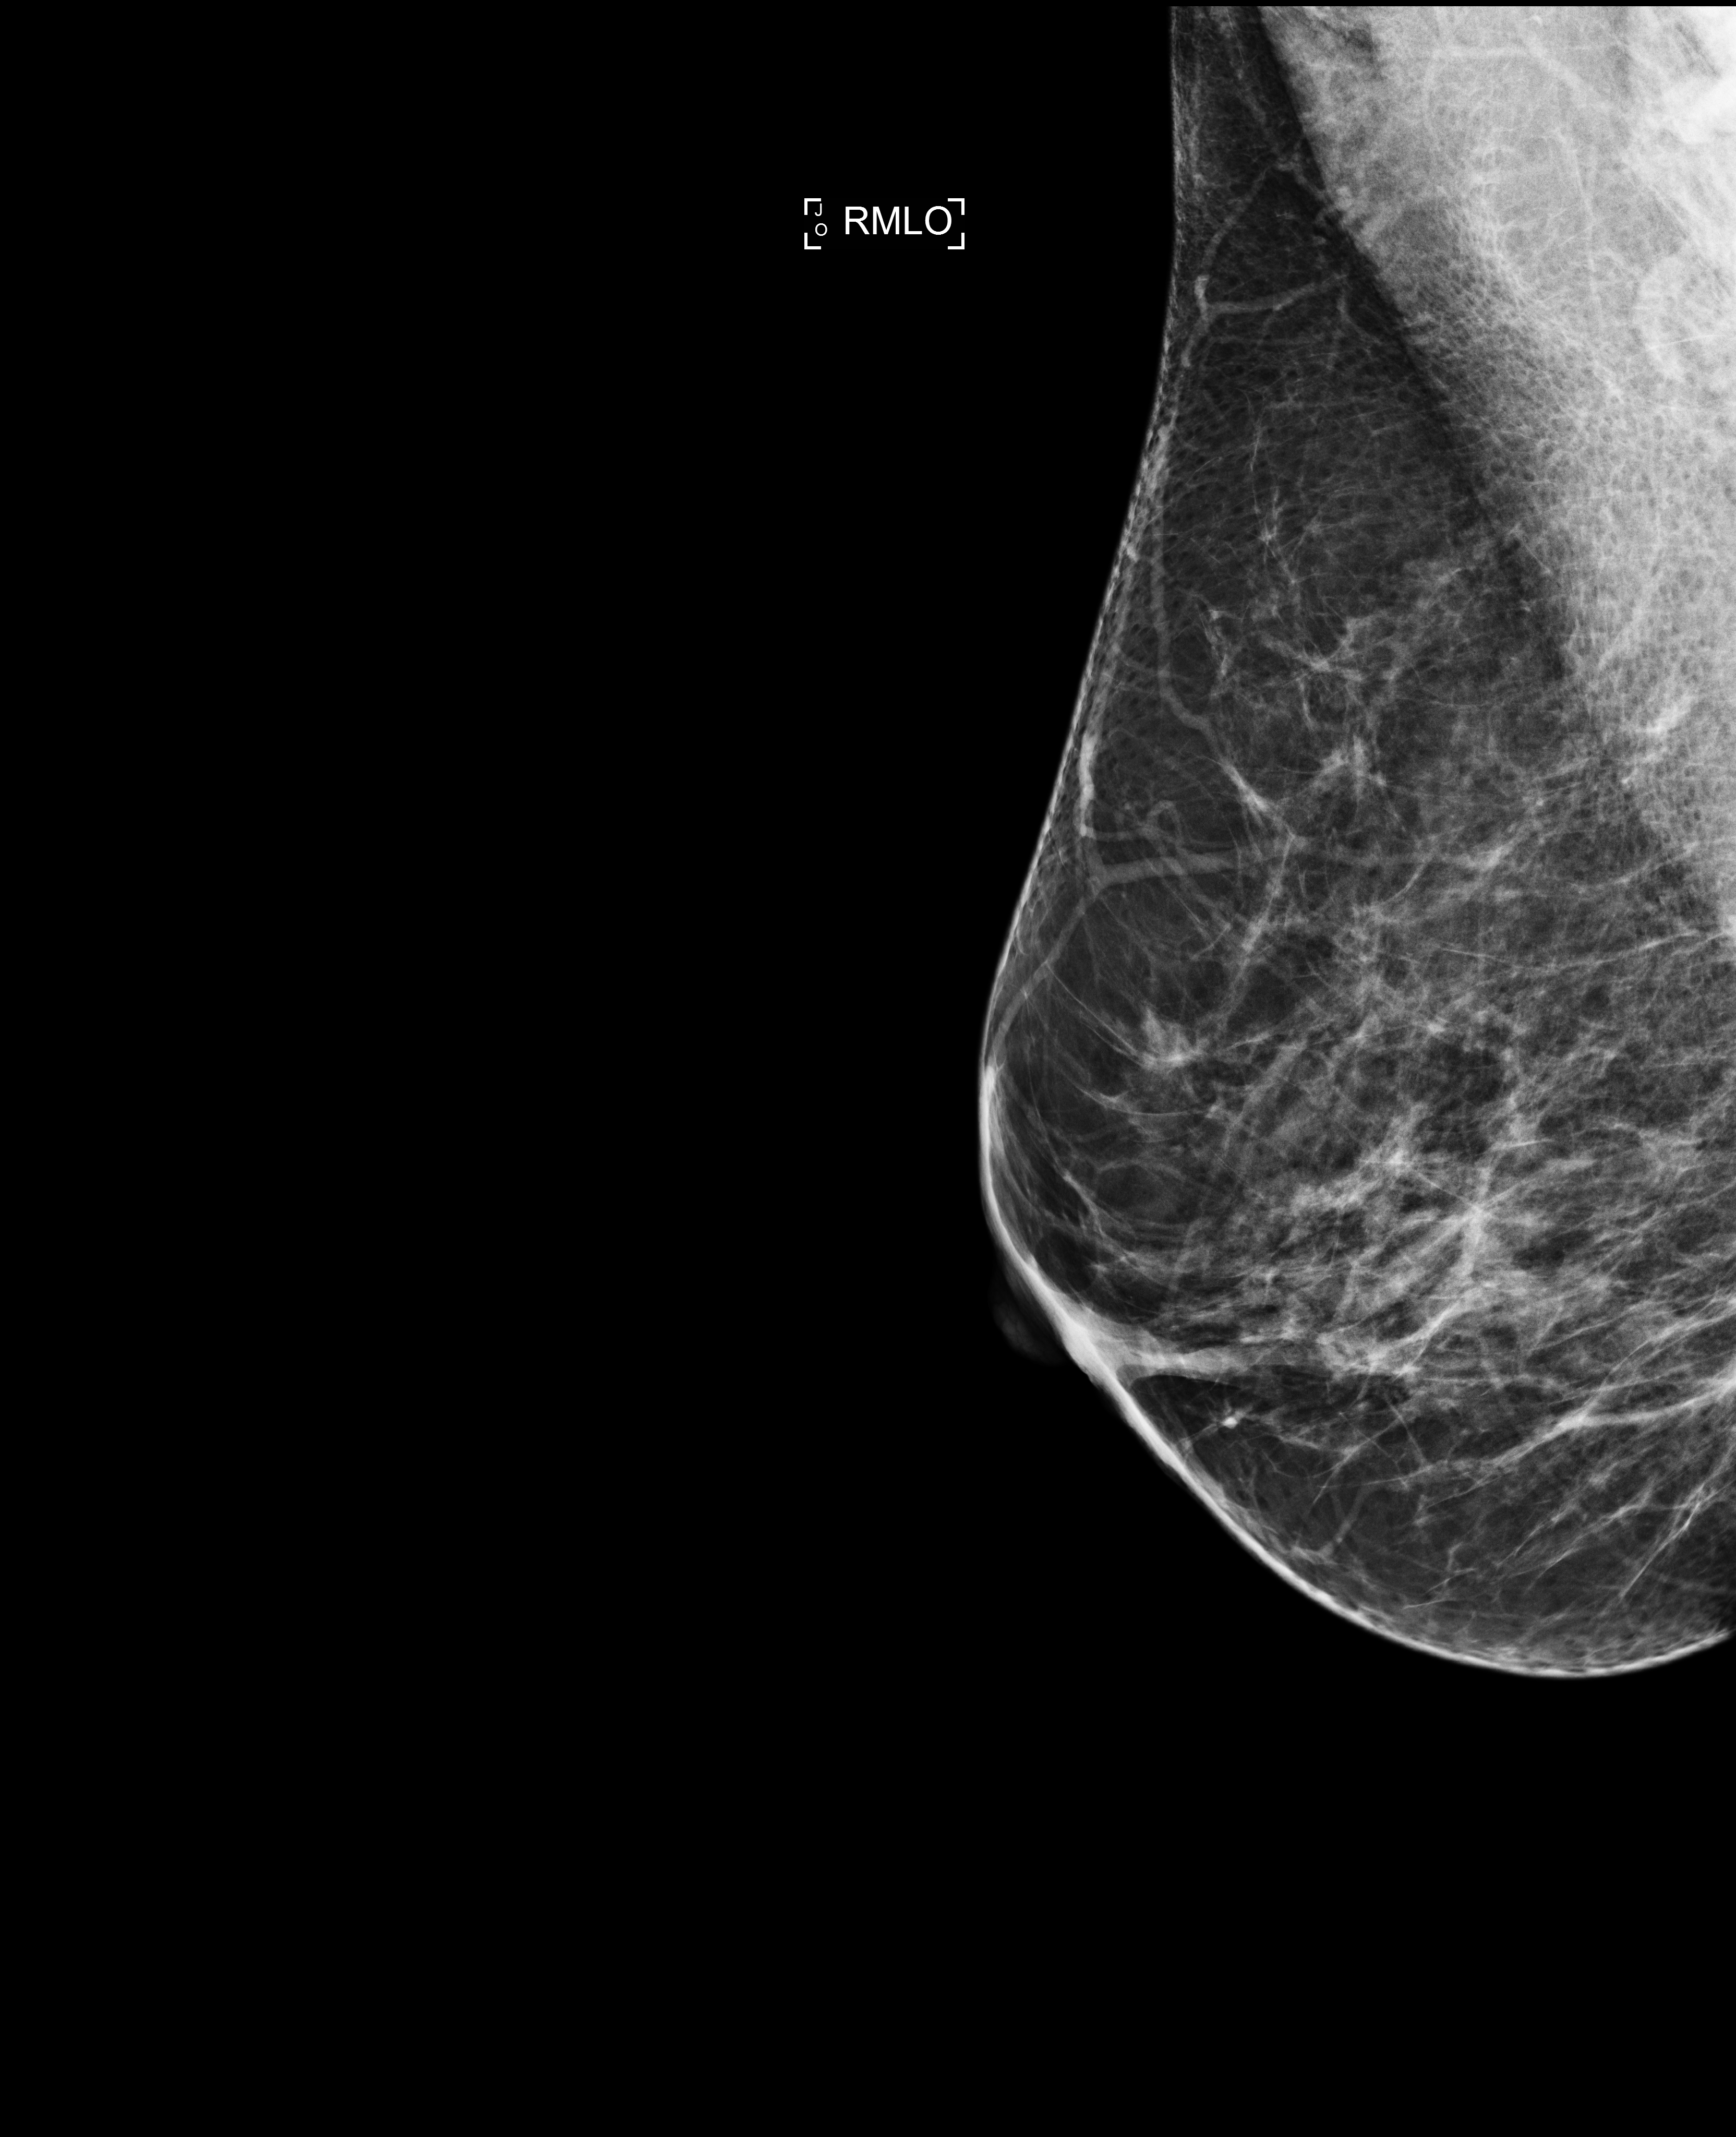
Screening examination. Patient aged 48 years (female).
Image type: full-field digital mammogram. Breast: right. Projection: medio-lateral oblique projection.